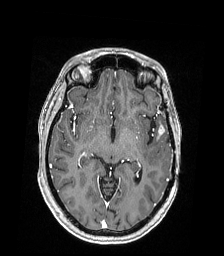
Brain MRI from a brain-tumour surgery series, one axial slice. Position 108 of 168 along the scan axis. T1-weighted post-contrast. 224 × 256 image matrix, field of view 224 × 256 mm. Case-level facts recorded for this patient, not image findings: histopathology: Astrocytoma; WHO grade: 4; IDH mutation: yes.
Annotated regions visible in this slice (expert manual segmentation):
- tumour: bounding box [x1, y1, x2, y2] px = [151, 121, 166, 140]